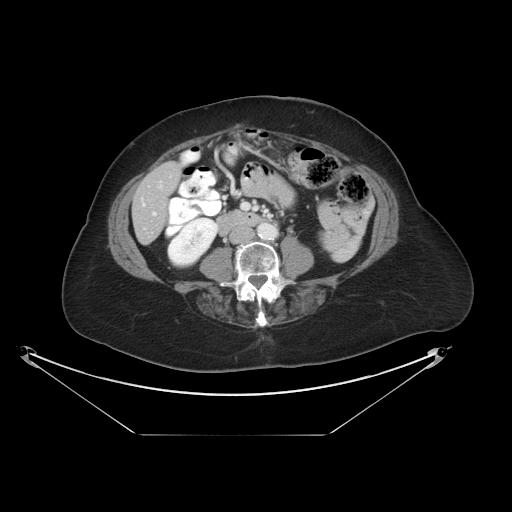
Contrast-enhanced abdominal CT, one axial slice; reconstruction kernel STANDARD; 120 kVp; intravenous contrast given; soft-tissue window (W 400 / L 40 HU); 5 mm slice thickness; 512 × 512 image matrix. Female patient, age 70 years. Case-level facts recorded for this patient, not image findings: diagnosis: colorectal cancer liver metastases, imaged before liver resection; multiple liver metastases: no; largest metastasis: 2.5 cm; disease in both lobes: no.
Structures marked on this image (outlined manually by an expert reader):
- hepatic veins: box from (x=143, y=204) to (x=145, y=206) px
- liver: (x=133, y=163)–(x=180, y=243)